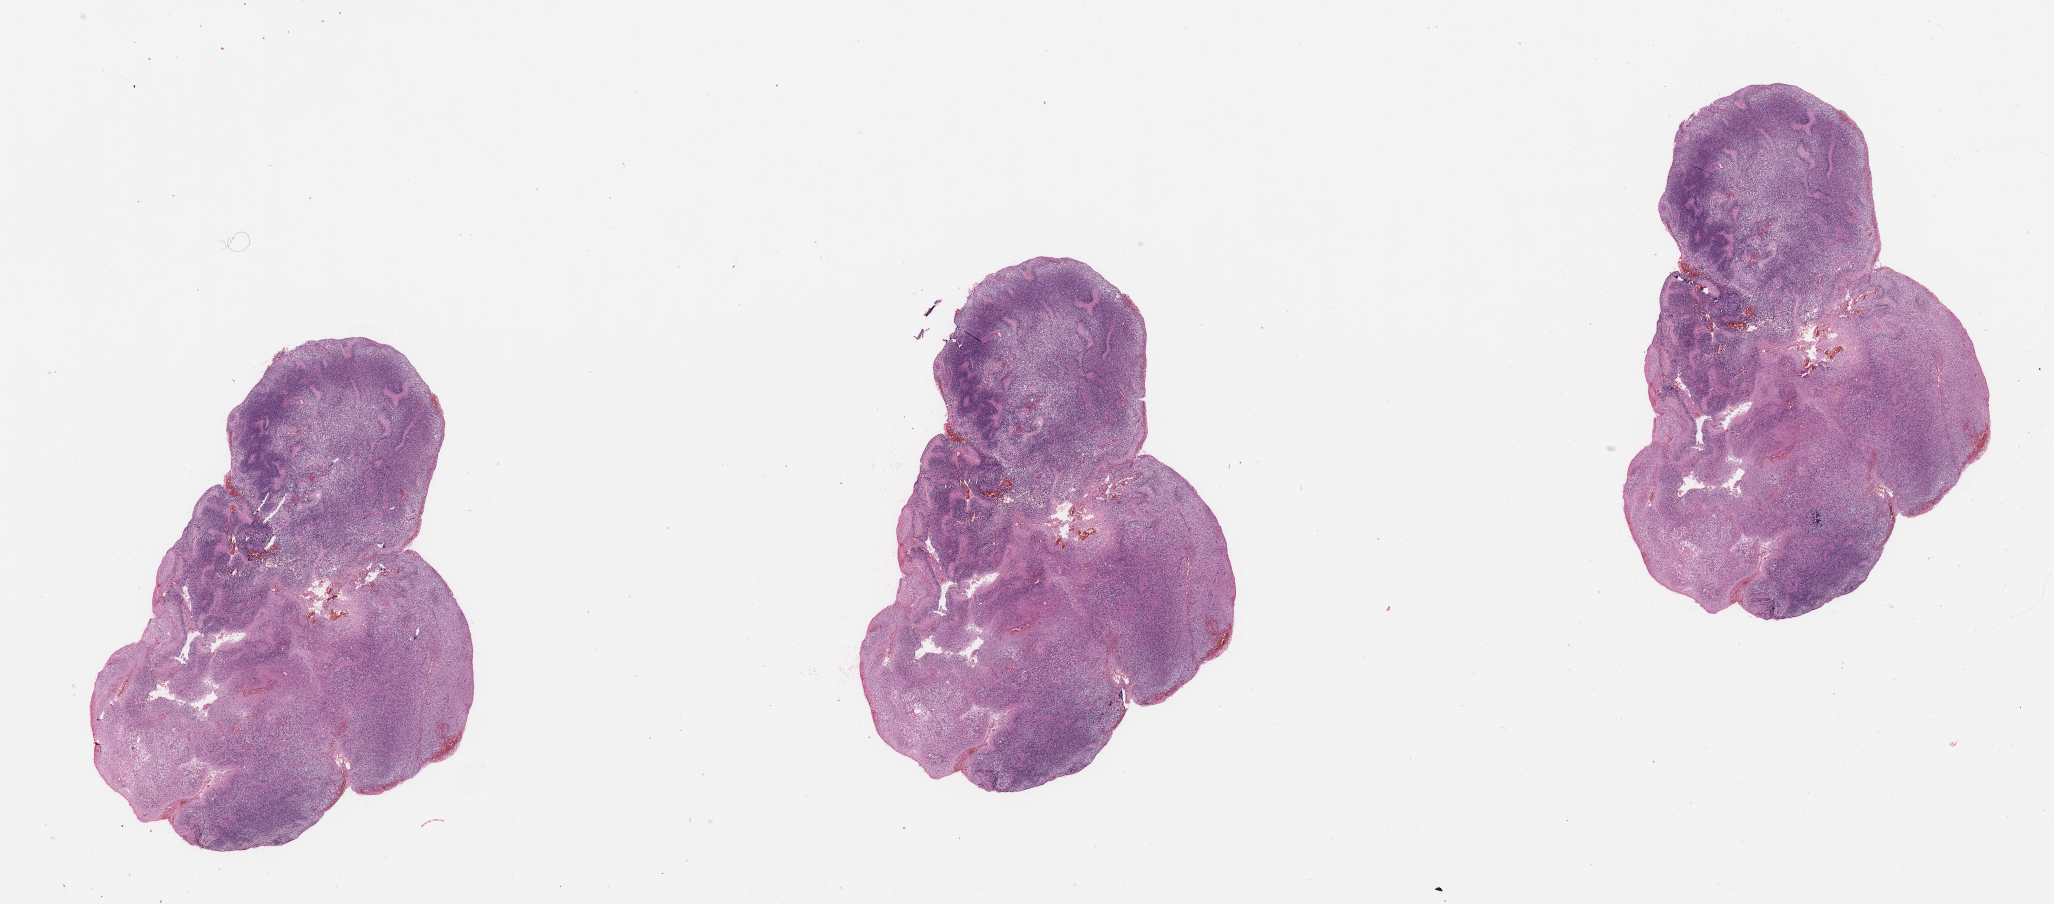
H&E whole-slide image, low-resolution overview of the scanned area, about 32.5 x 14.3 mm. Brain, tumour tissue. Female, 68 y/o.
Histologic diagnosis: Glioblastoma. Primary tumour site (as recorded): parietal lobe.